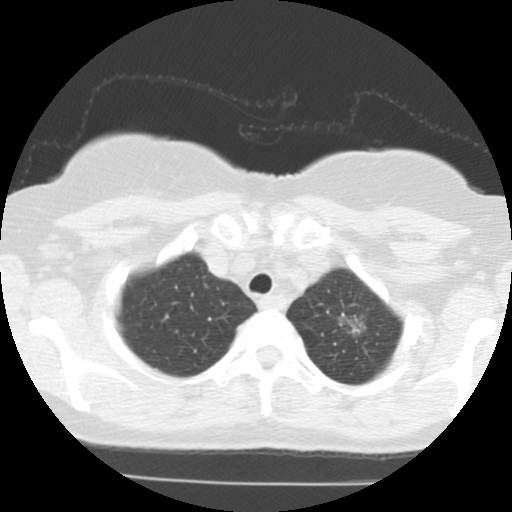
Low-dose screening chest CT, one axial slice; slice 103 of 123 in the series (ordered by position); reconstruction kernel STANDARD; lung window (W 1500 / L -600 HU); 2.5 mm slice thickness; 512 × 512 image matrix, field of view 290 × 290 mm.
Annotated regions visible in this slice (manually delineated by an expert):
- lesion 1 (tumor, upper lobe of left lung): bounding box (x1, y1, x2, y2) in pixels: (340, 313, 367, 334)